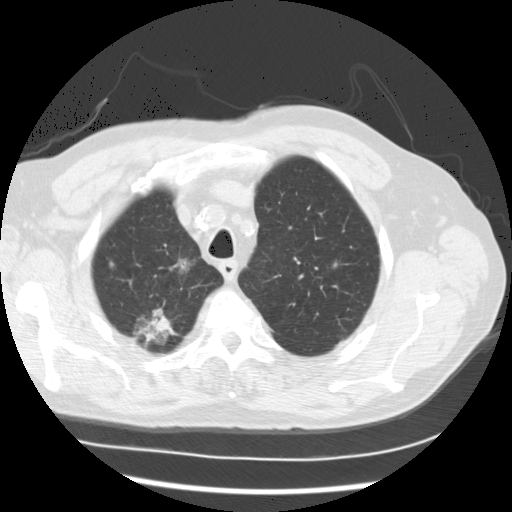
Axial slice from a low-dose chest CT screening exam. First (baseline) screen. Lung window (W 1500 / L -600 HU). 2.5 mm slice thickness. 512 × 512 image matrix, field of view 360 × 360 mm. Male participant, aged 68 years at enrolment. Current smoker at enrolment.
• Lesion marked by an expert reader, bounding box [x1, y1, x2, y2] px = [115, 290, 191, 360].
• The screening reader recorded 3 non-calcified nodules or masses ≥4 mm on this exam; which of them this box marks is not recorded.
• Lung cancer was diagnosed 90 days after this screen: adenocarcinoma, NOS, right upper lobe, right lower lobe, well differentiated (G1), stage IV (AJCC 6th edition), 35 mm at pathology.